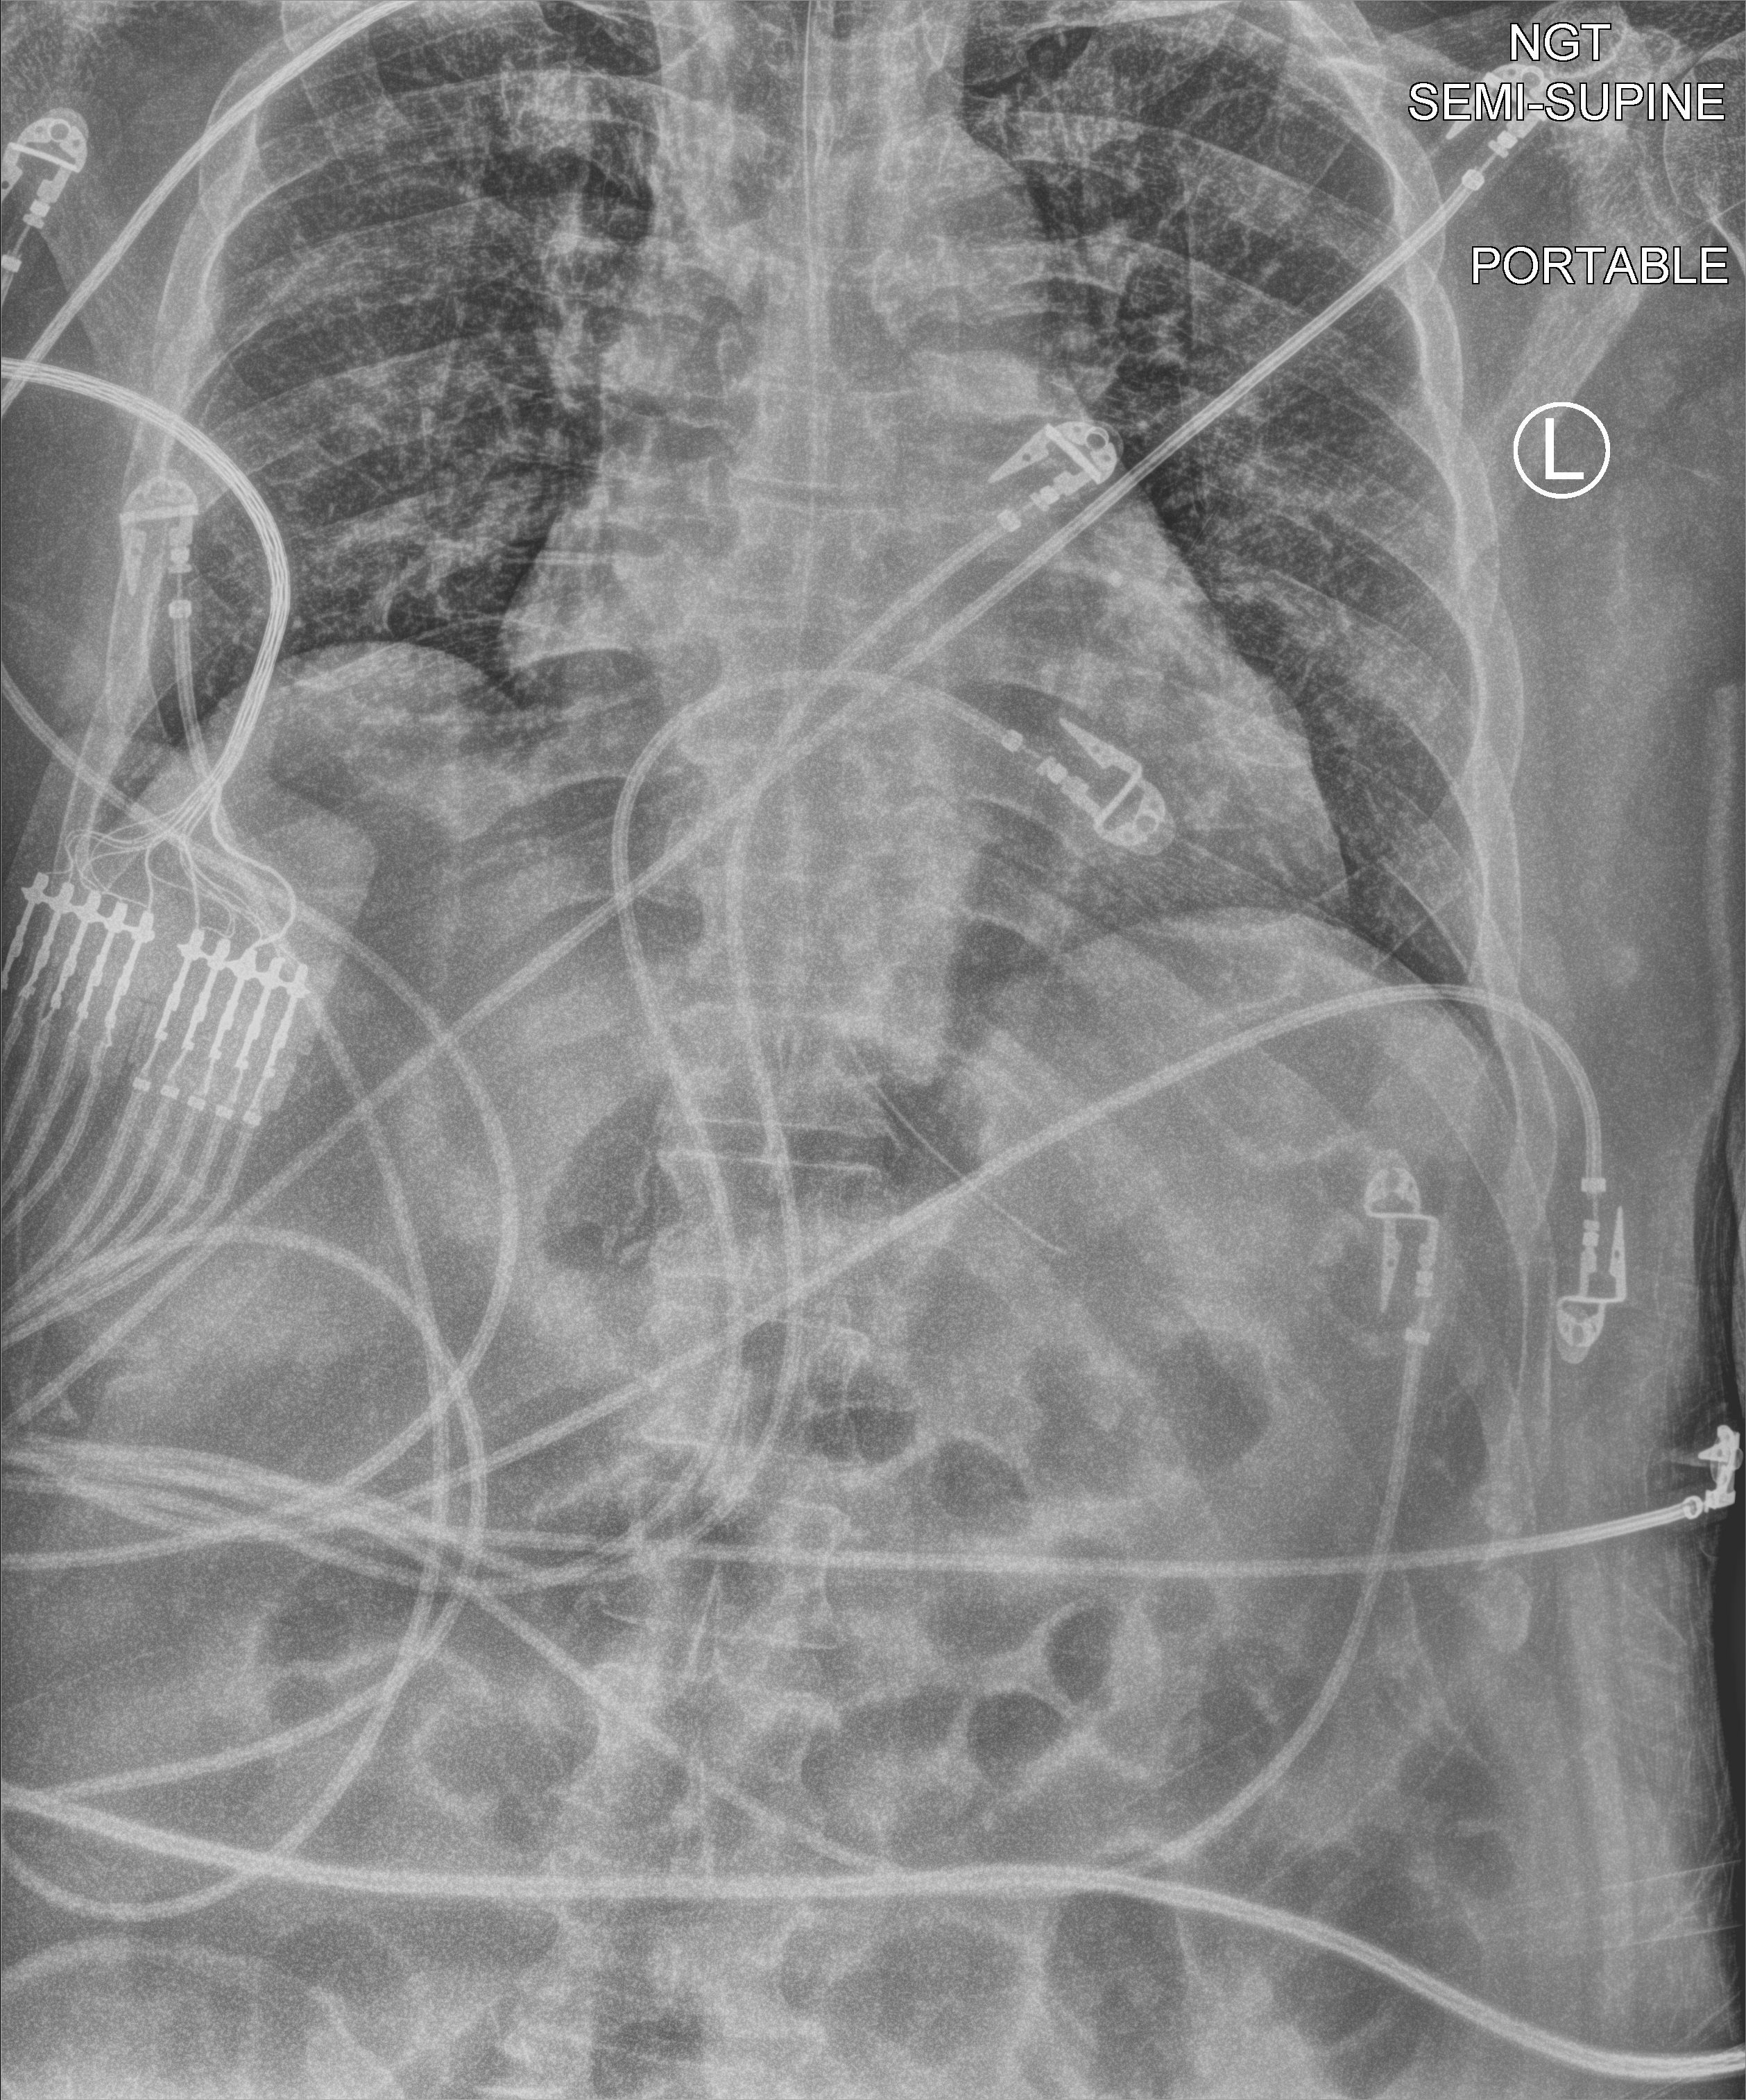
Portable chest radiograph; anteroposterior (AP) projection. Adult patient hospitalised with COVID-19, age 18–59 years.
Hospital-stay facts (about this admission, not read from this image; timing relative to this image not recorded): other chronic lung disease (admission record): no.